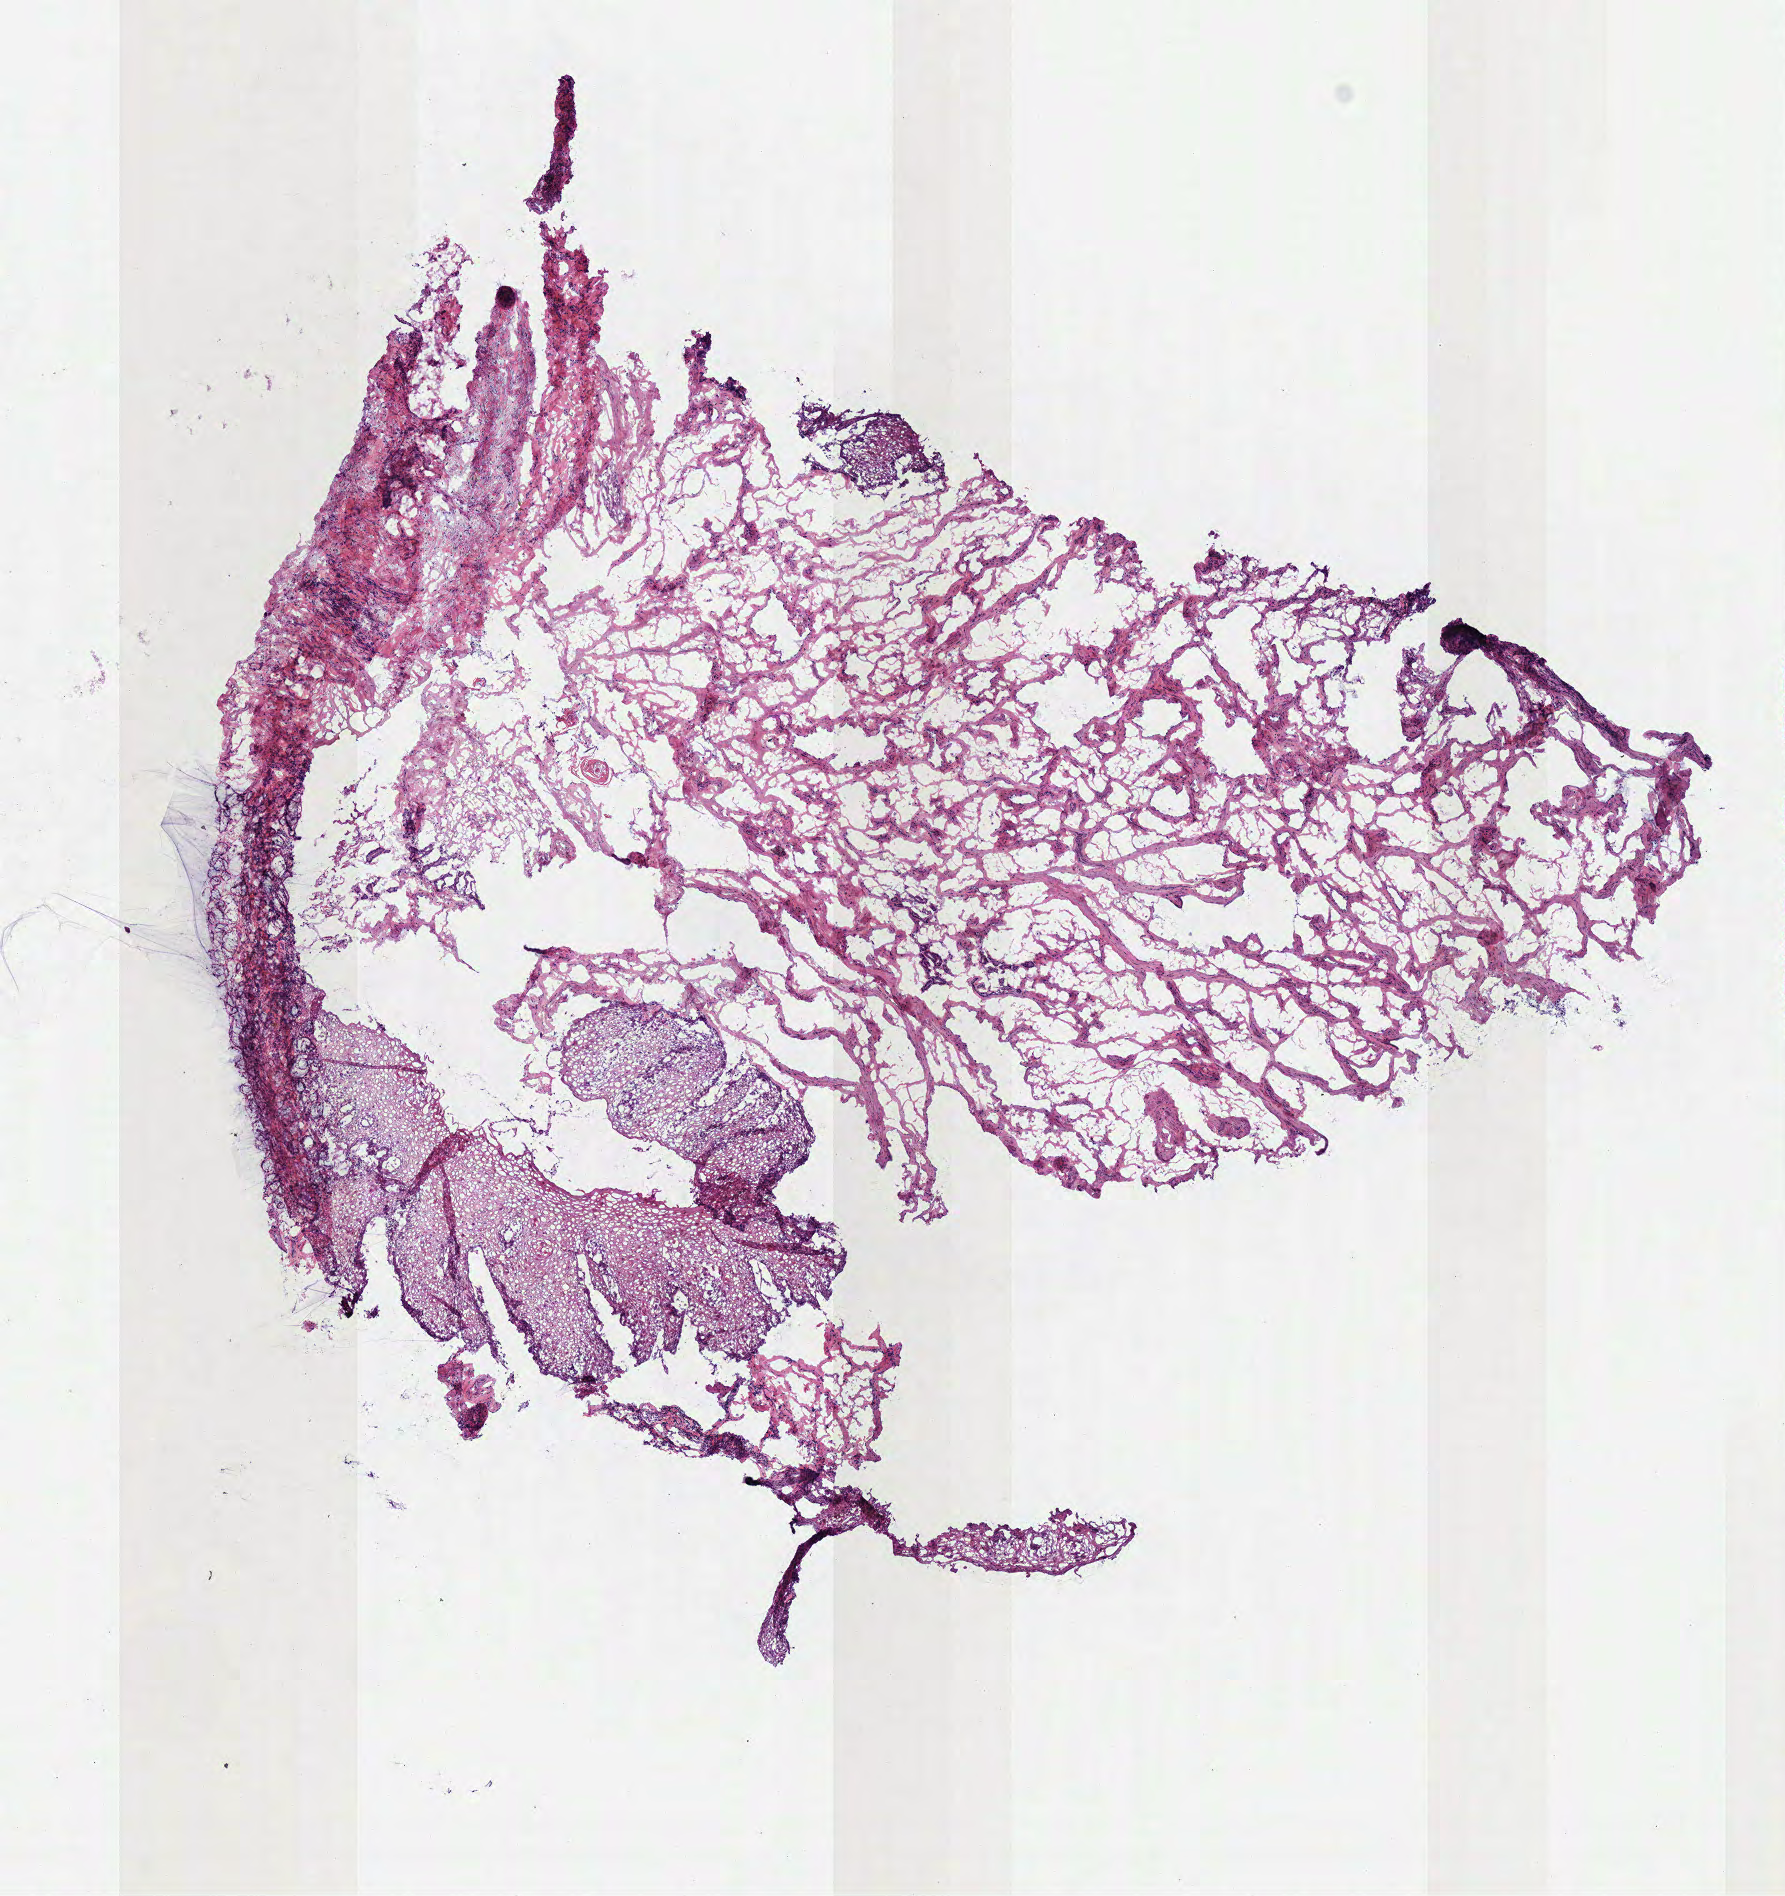
Whole-slide histology image, H&E, a low-resolution overview of the entire scanned area, about 7.0 x 7.5 mm; frozen section; head and neck, solid tissue normal (non-tumour tissue) sample. Female patient; age at initial diagnosis 74 years.
This section: solid tissue normal (non-tumour) sample from the same patient. Patient diagnosis: Squamous cell carcinoma, NOS (overlapping lesion of lip, oral cavity and pharynx).